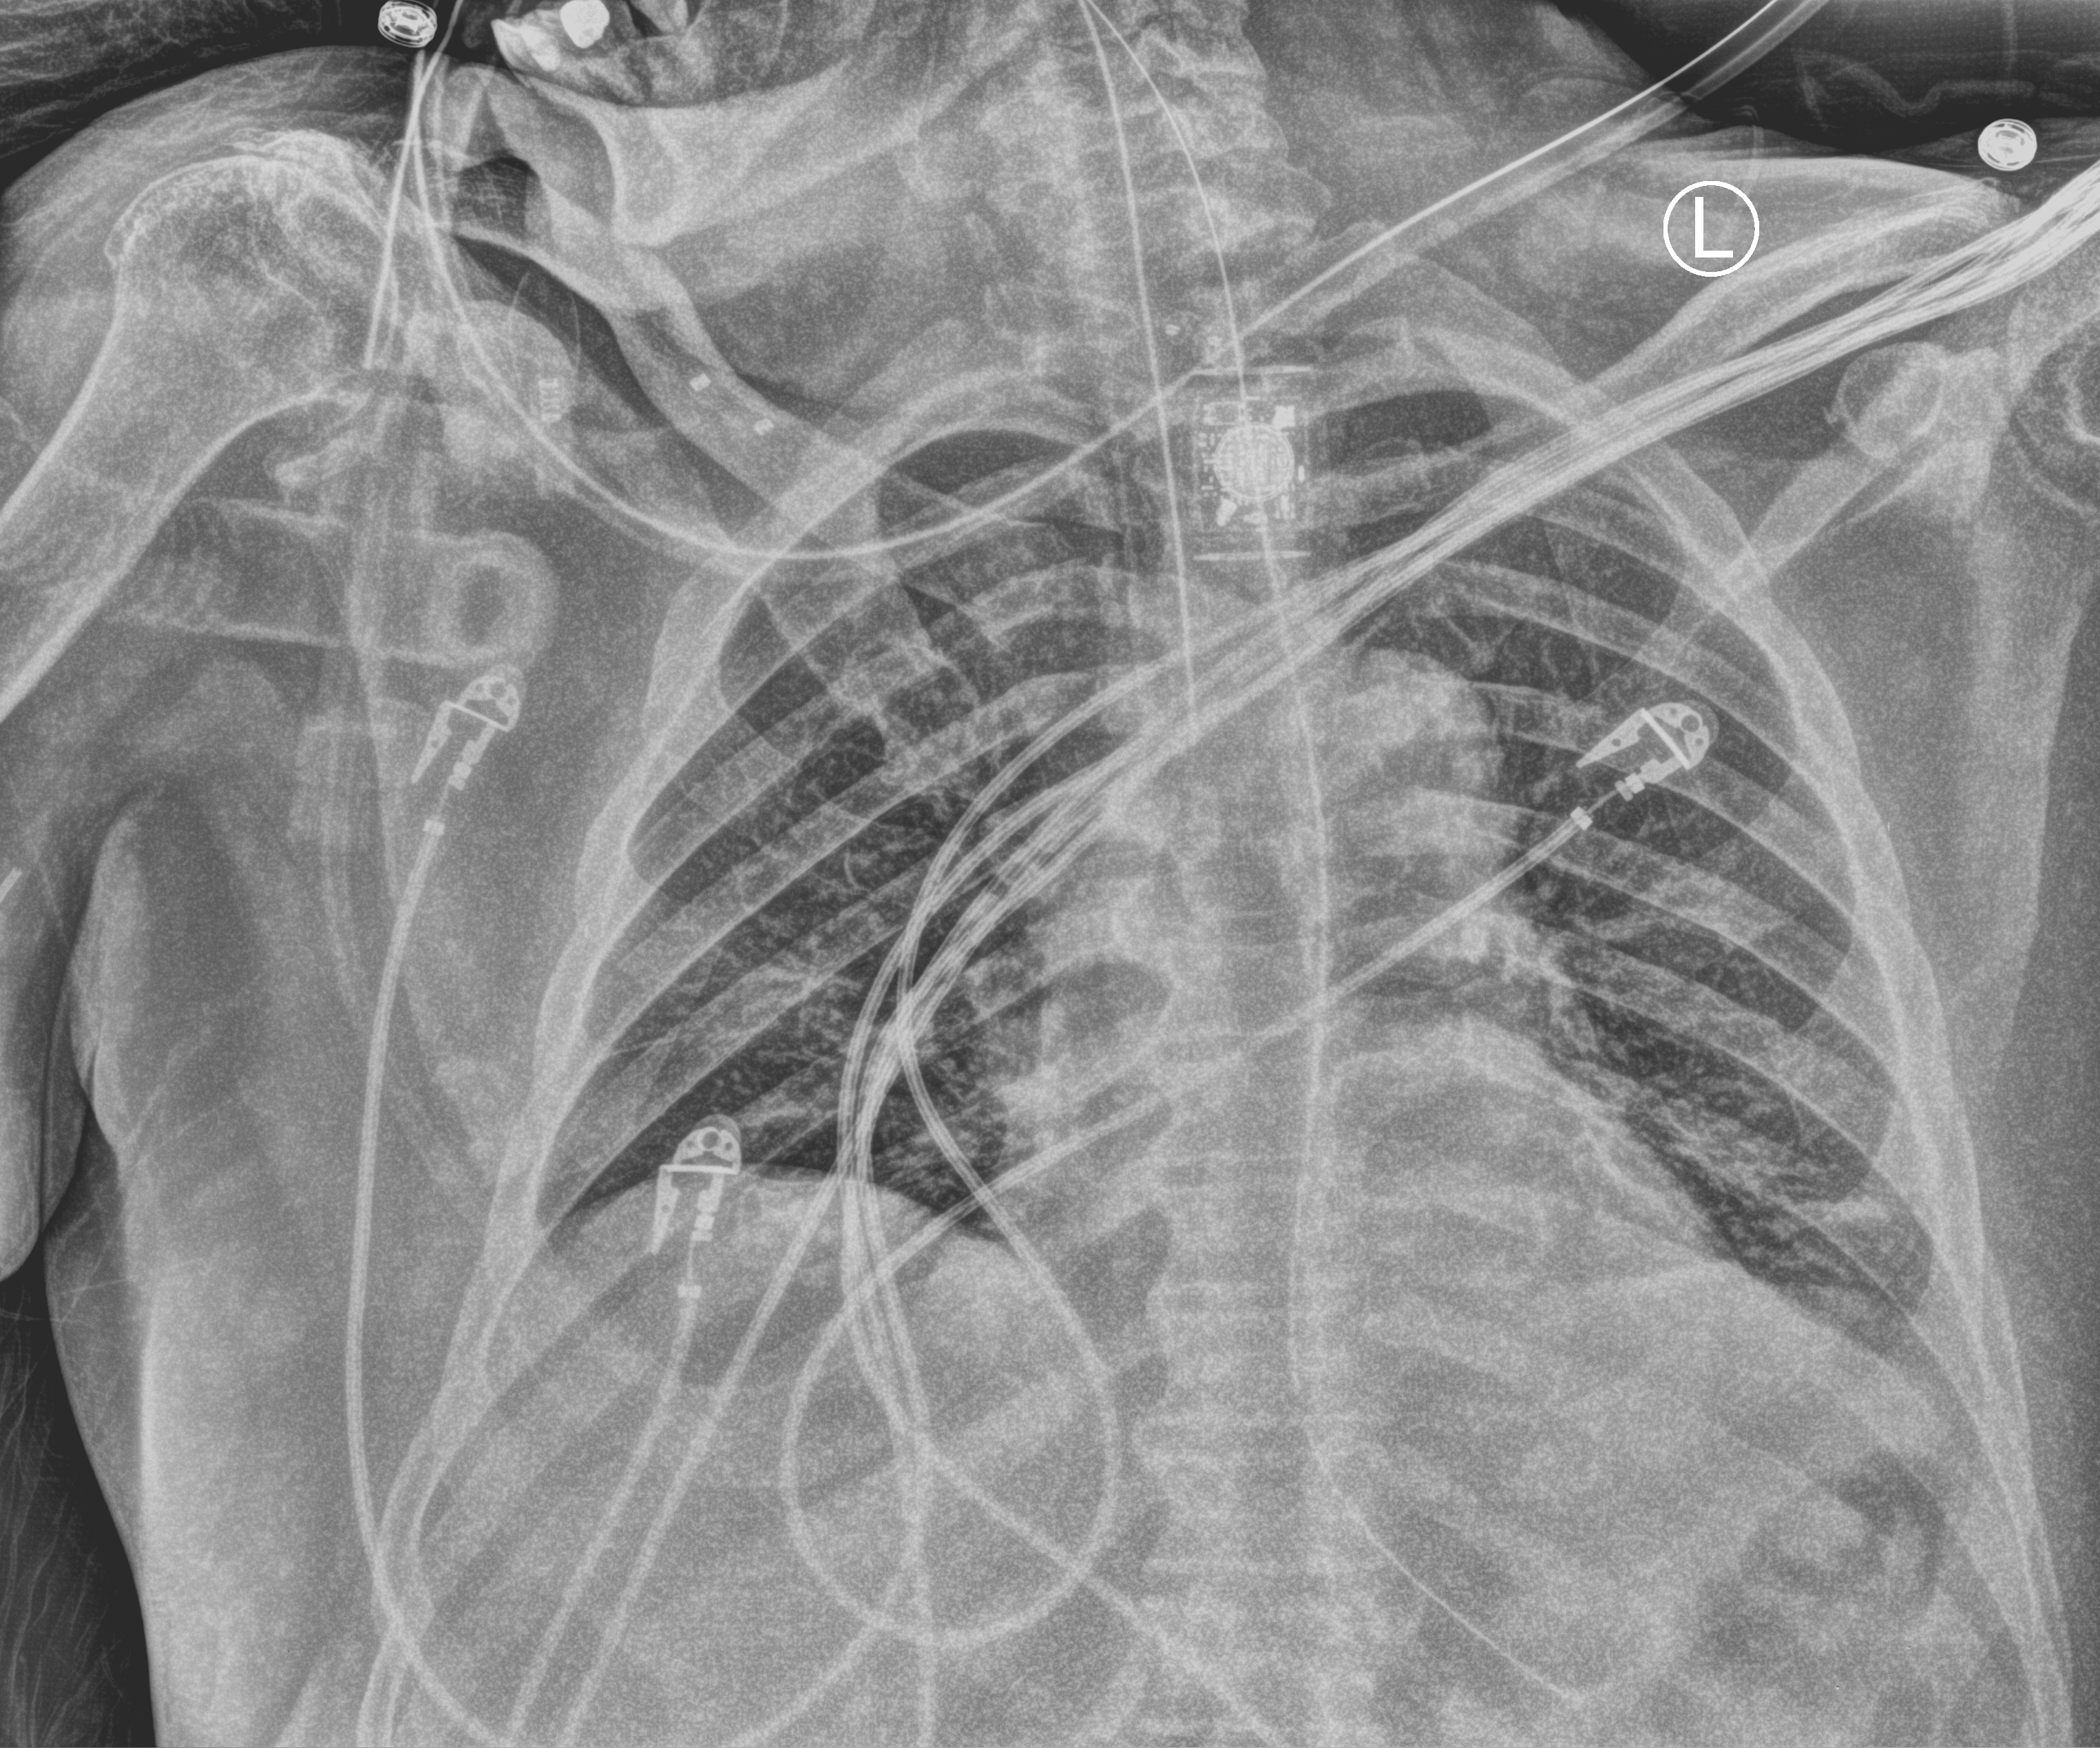
Bedside chest radiograph (computed radiography); anteroposterior (AP) projection. Patient hospitalised with COVID-19; male, aged 75–90 years.
Admission-level facts for this patient (not findings on this image; timing relative to this image not recorded): mechanically ventilated during this hospital stay: yes.